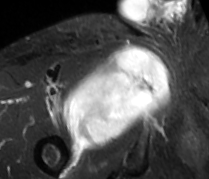
MRI of an extremity soft-tissue mass, one axial slice; position 61 of 89 along the scan axis; STIR; MR volume resampled by the dataset authors to the PET/CT grid (not the native acquisition matrix); 3.27 mm slice thickness; 209 × 179 image matrix. Male patient. Case-level facts recorded for this patient, not image findings: histological type: undifferentiated - pleiomorphic; grade: high; site of the primary tumour: right thigh.
Outlined on this slice (expert contour drawn on MRI and transferred to this co-registered scan by the dataset authors):
- gross tumour volume including surrounding oedema: bounding box (x1, y1, x2, y2) in pixels: (62, 46, 170, 150)
- gross tumour volume (mass): (62, 46, 170, 150)